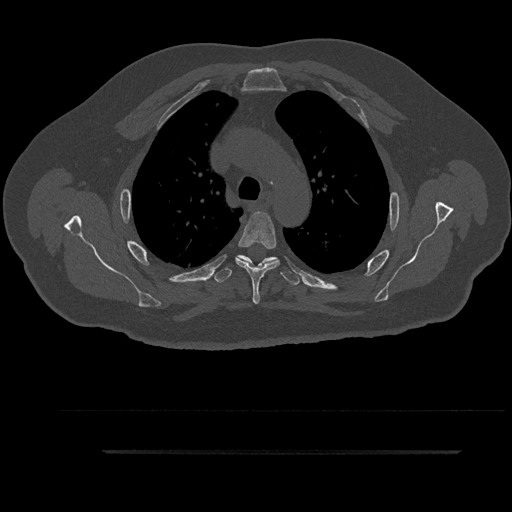
CT including the spine, one axial slice. Slice 662 of 797 in the series (ordered by position). 120 kVp. Bone window (W 1800 / L 400 HU). 512 × 512 image matrix. Male patient, age 63 years. Case-level facts recorded for this patient, not image findings: primary cancer: renal; vertebrae with lytic lesions (as recorded): T8.
Annotated regions visible in this slice (semi-automatic segmentation, software-assisted and operator-edited):
- T4 vertebra: bounding box <235,212,280,304> (left, top, right, bottom; pixels)
- T5 vertebra: <213,255,300,286>